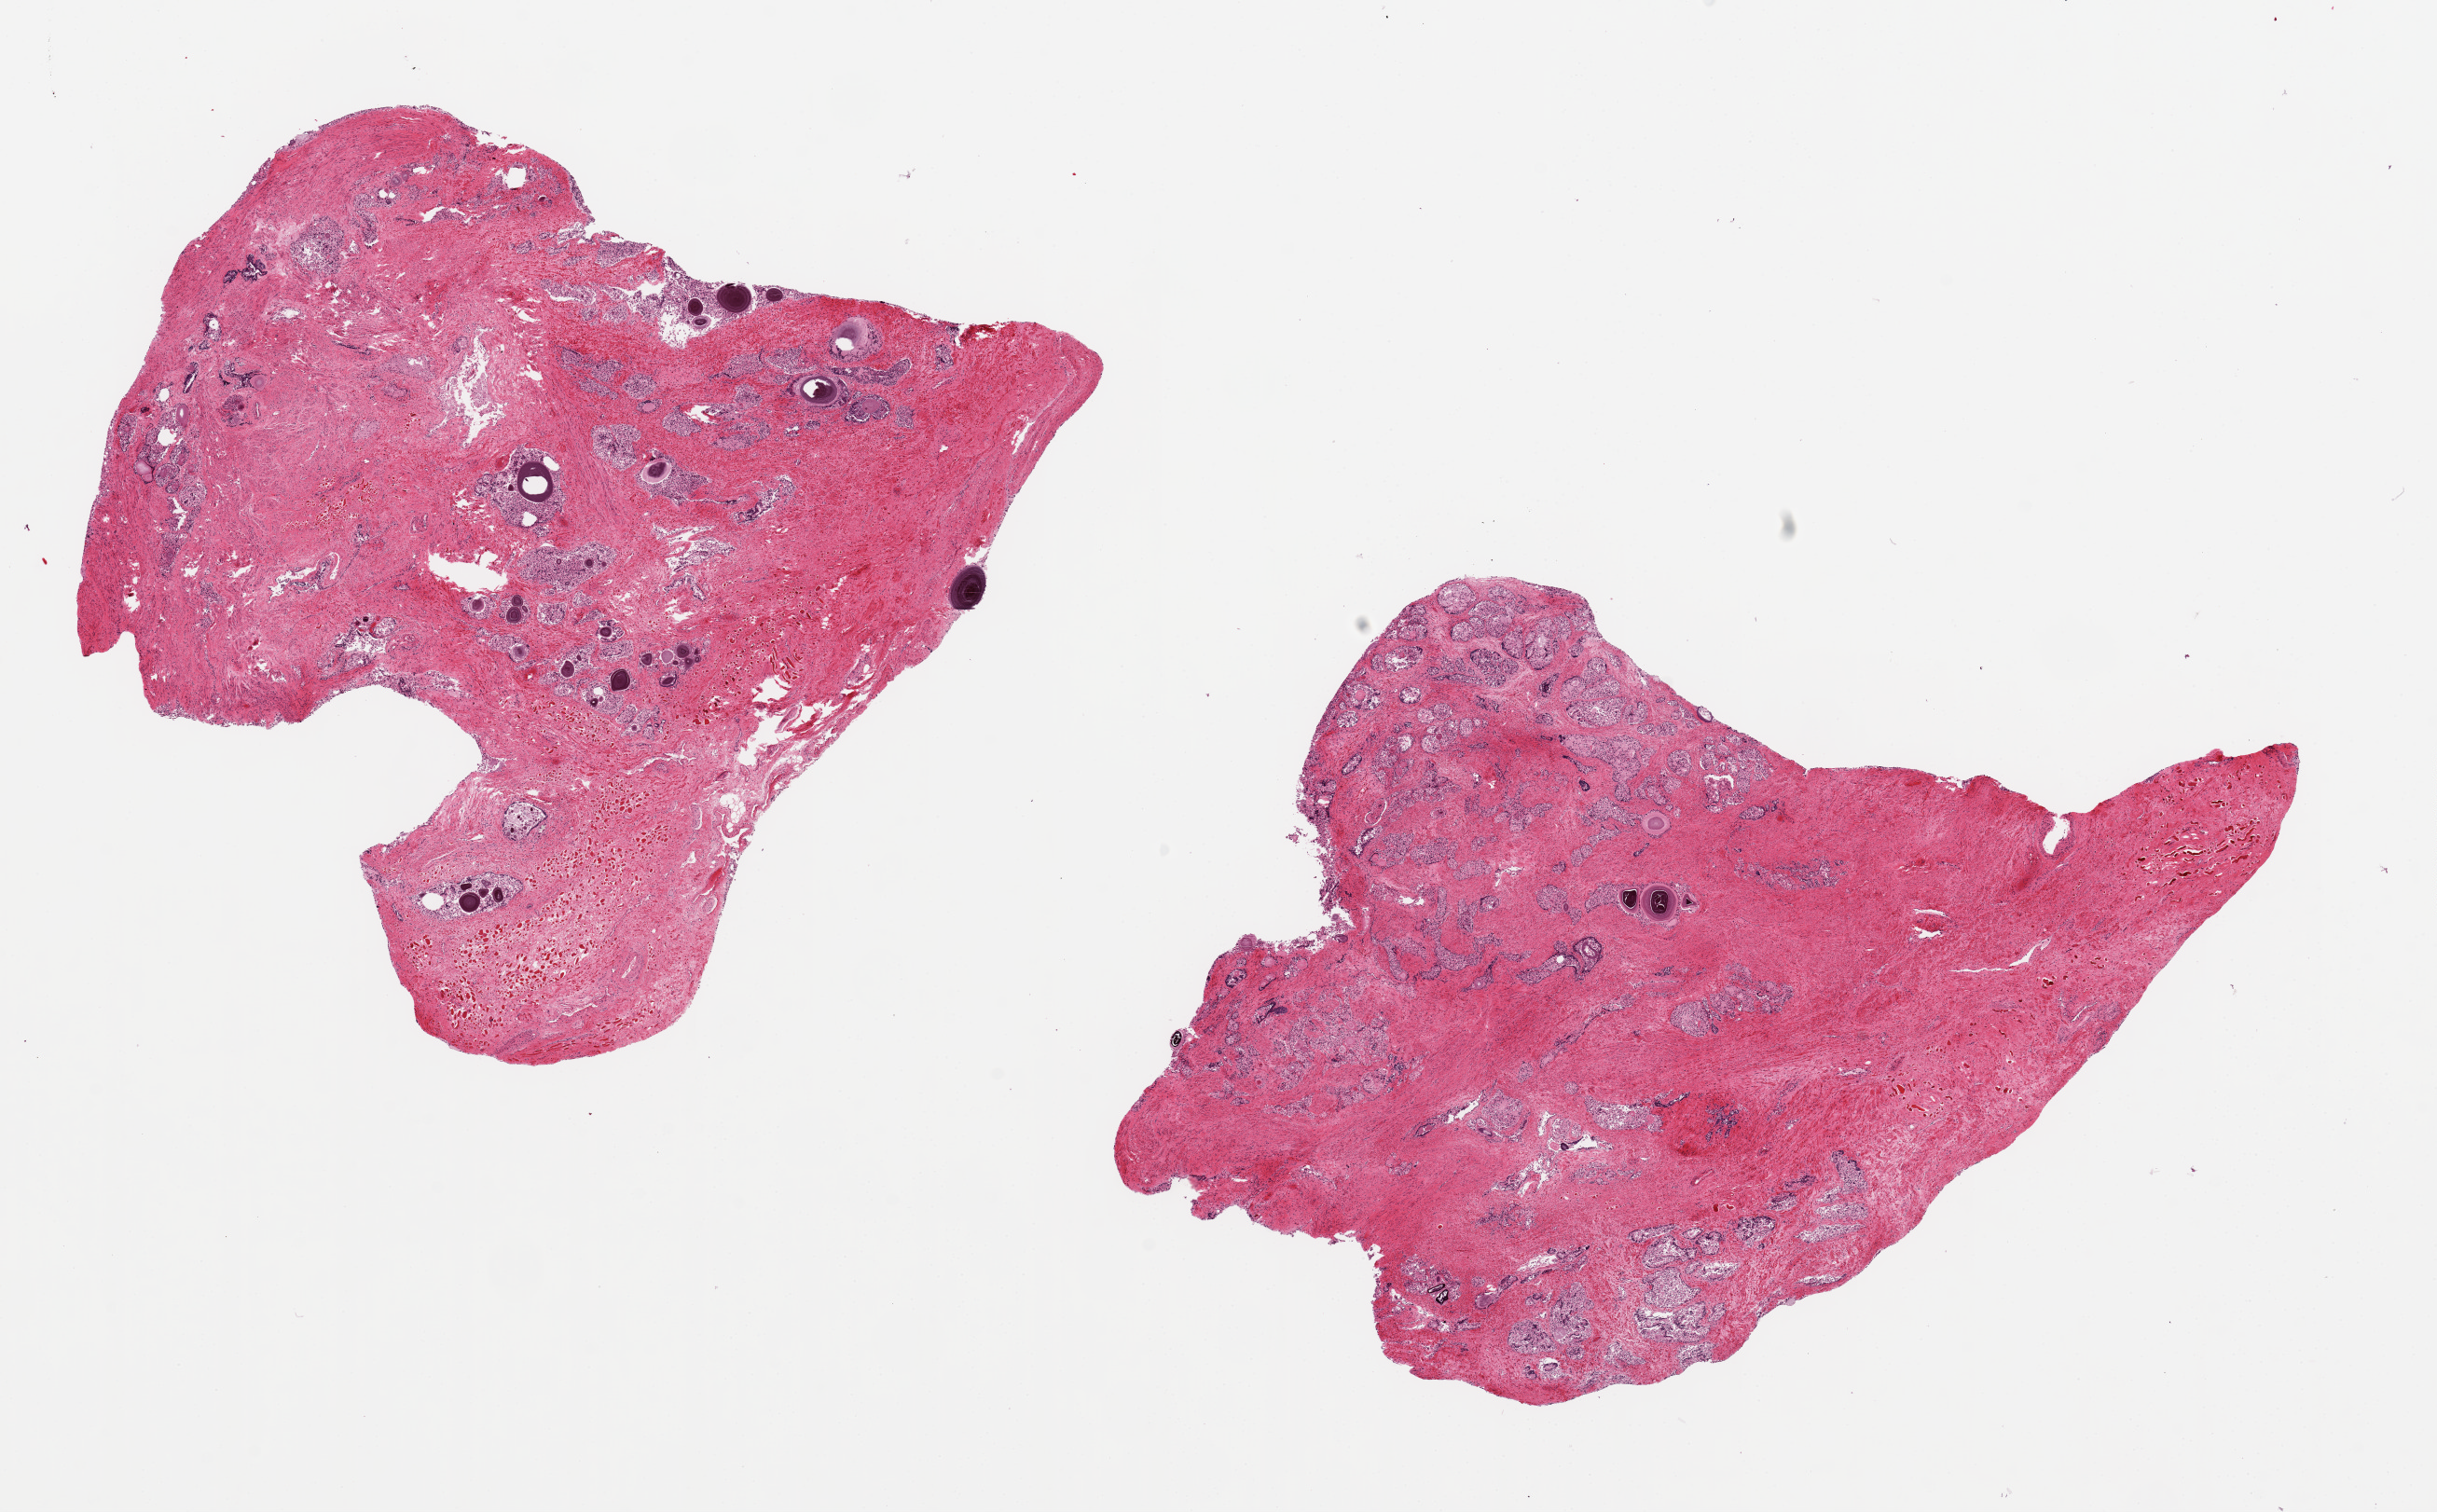
Hematoxylin and eosin (H&E) whole-slide image — low-resolution overview of the scanned area, about 20.7 x 12.8 mm. PAXgene-fixed, paraffin-embedded tissue. Section of prostate (target tissue). Tissue donor sample. Male donor.
• pathologist's review note for this sample: 2 aliquots, ~8x7mm. Glands with near-total autolysis, probable hyperplasia based on pattern